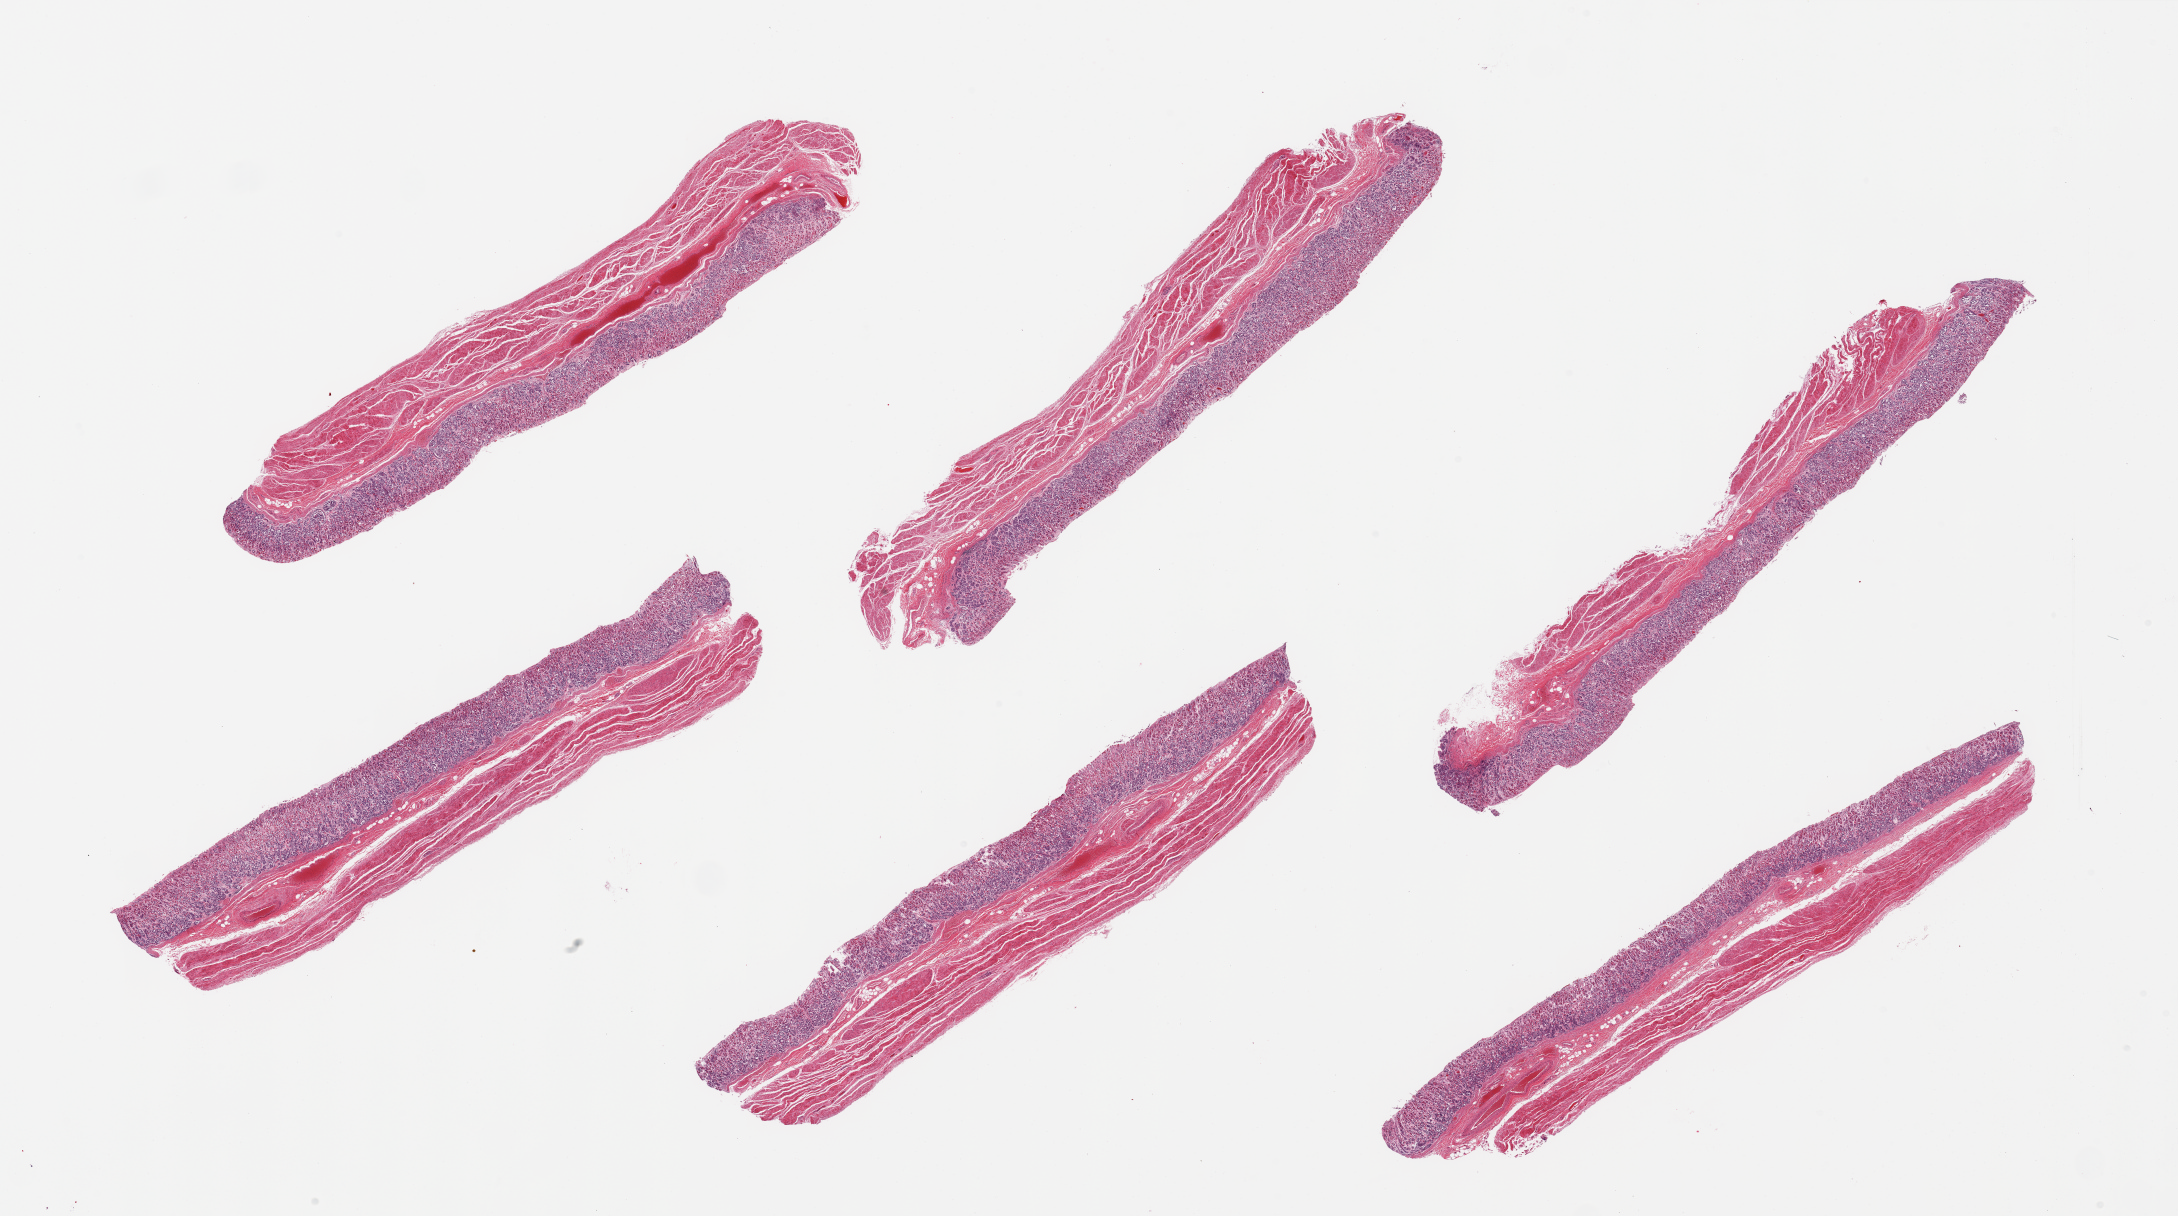
H&E whole-slide image, brightfield, low-resolution overview of the scanned area, about 34.5 x 19.2 mm; PAXgene-fixed paraffin-embedded (PFPE) section; target tissue: stomach; donor tissue sample. Donor: male.
Reviewer comment on this tissue sample: 6 pieces; well trimmed; mild to moderate mucosal autolysis.